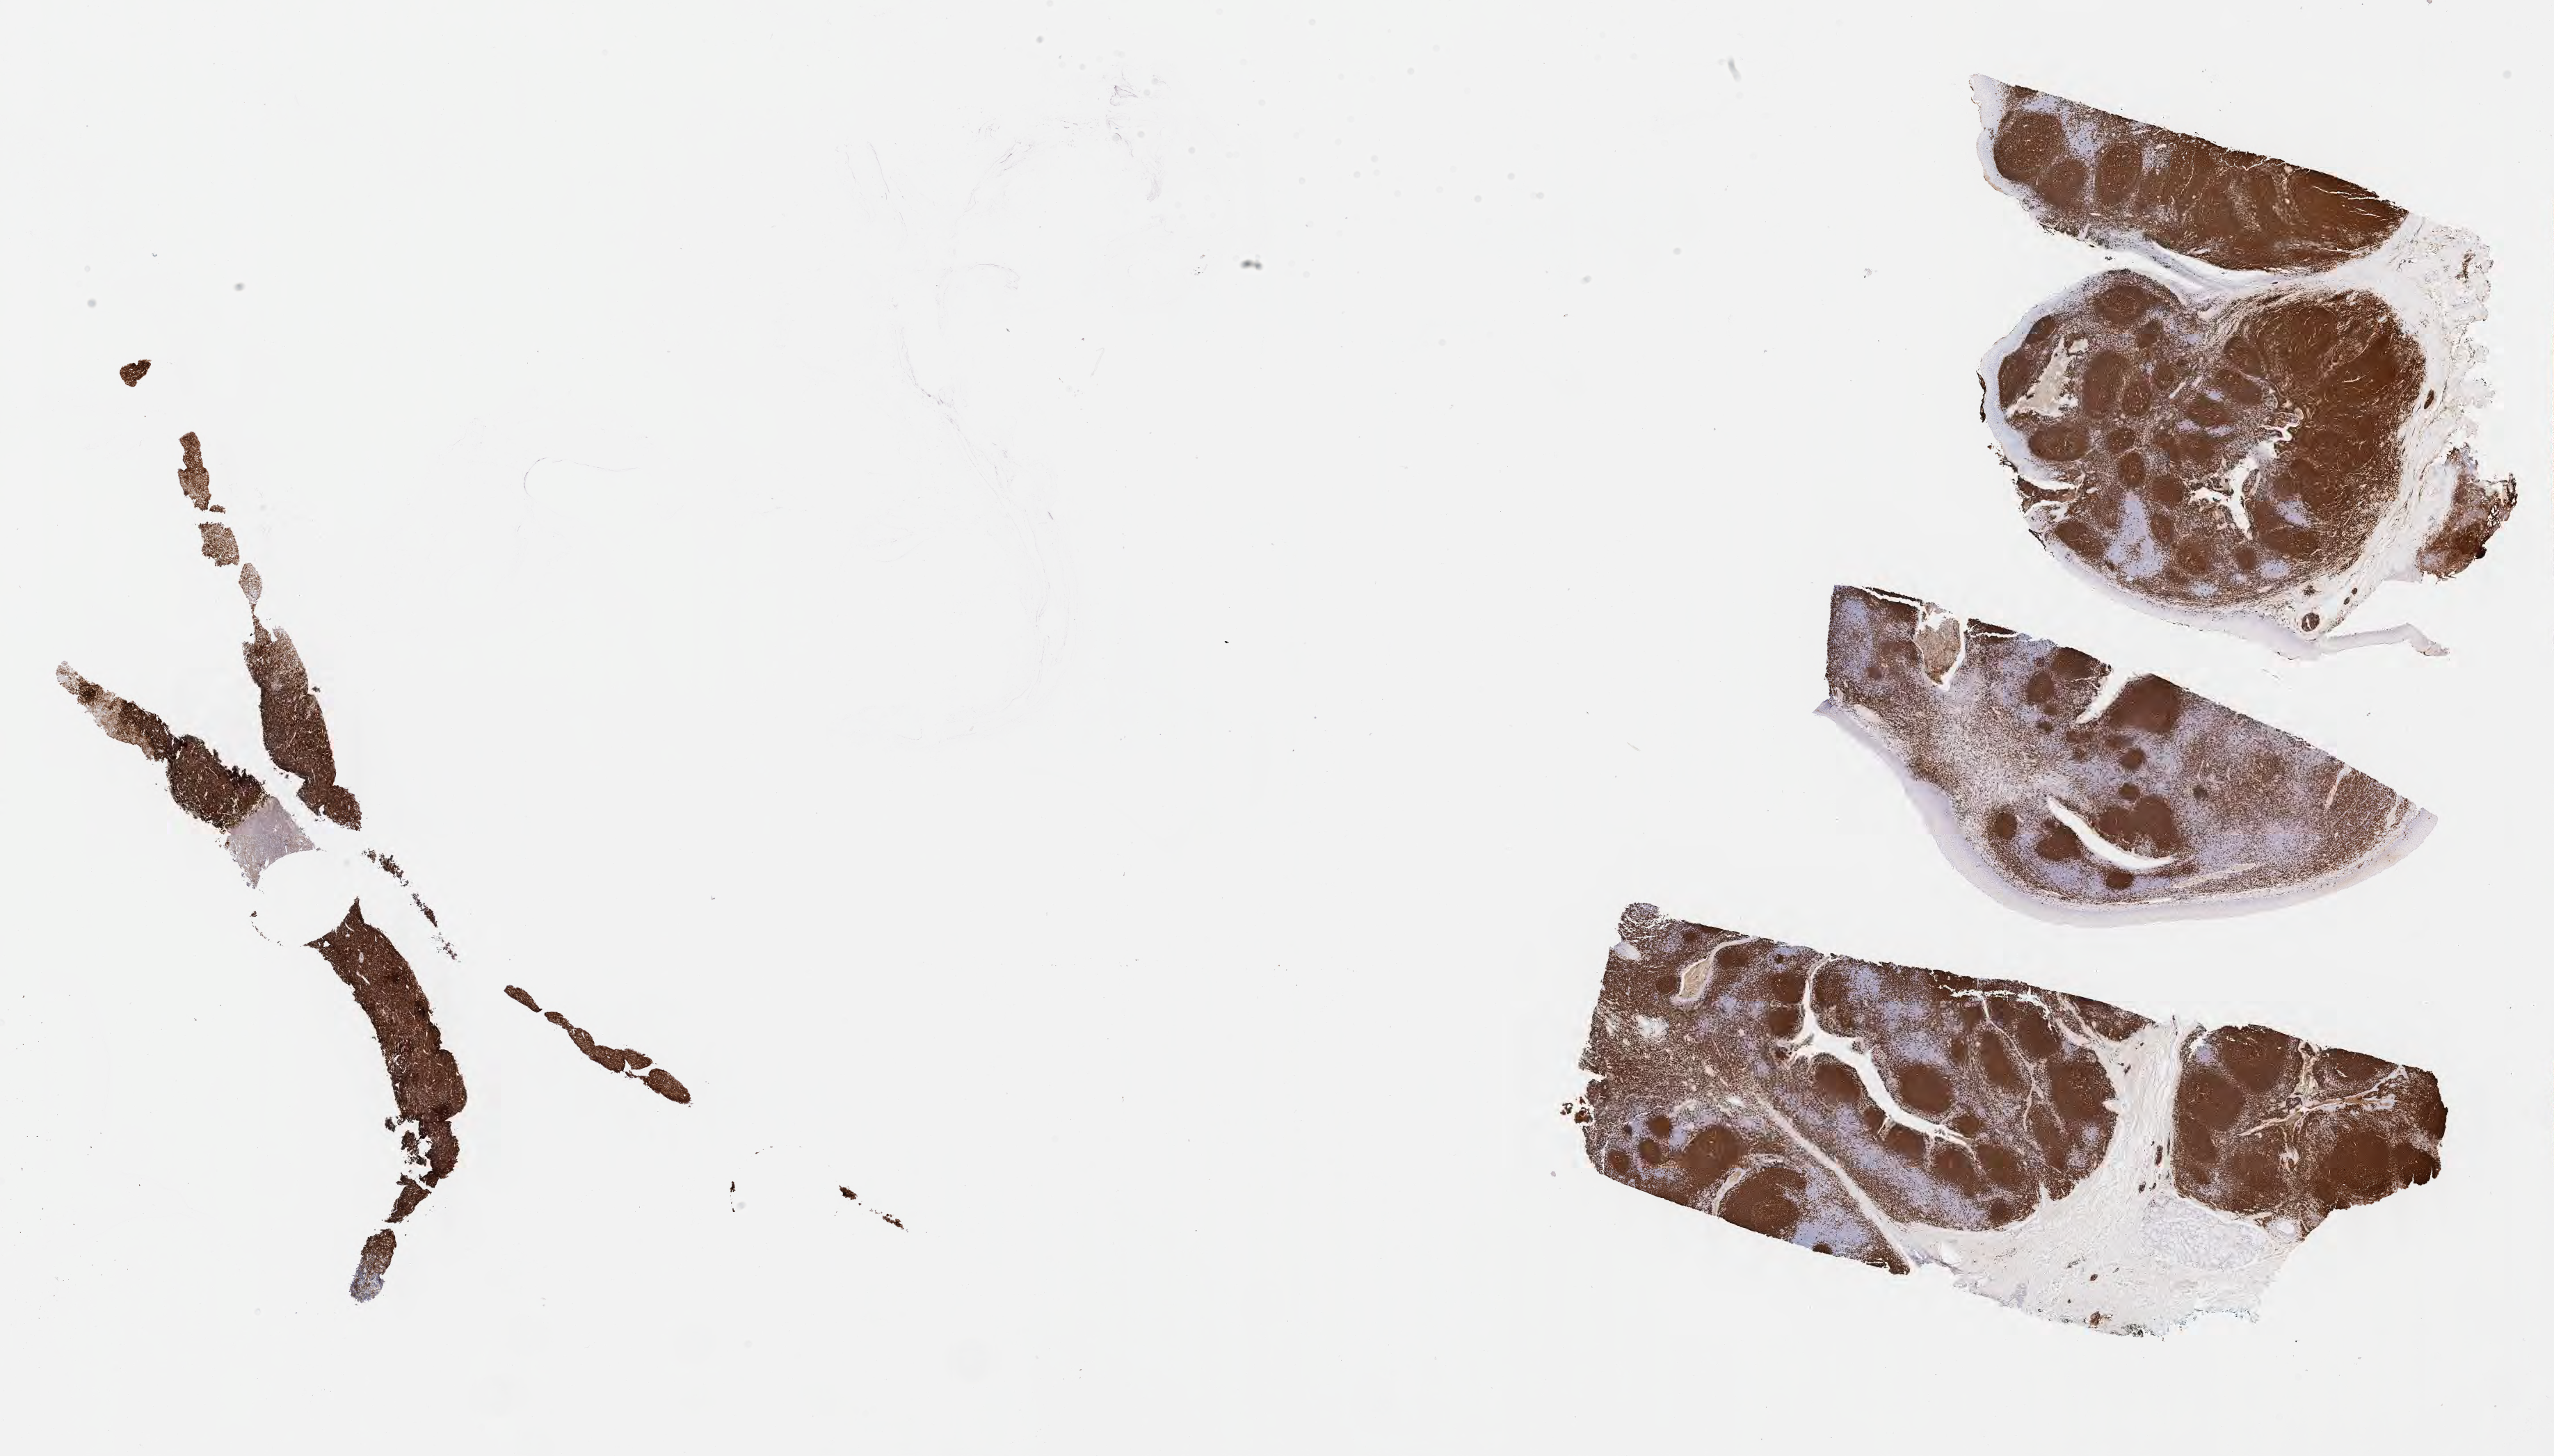
Immunohistochemistry (IHC) whole-slide image stained for CD20 — whole scanned area (about 29.7 x 16.9 mm) shown as a low-resolution overview. Specimen: tumor tissue. Site: abdomen proper. Patient: male, age 14 years.
Histologic diagnosis: Burkitt lymphoma, NOS.